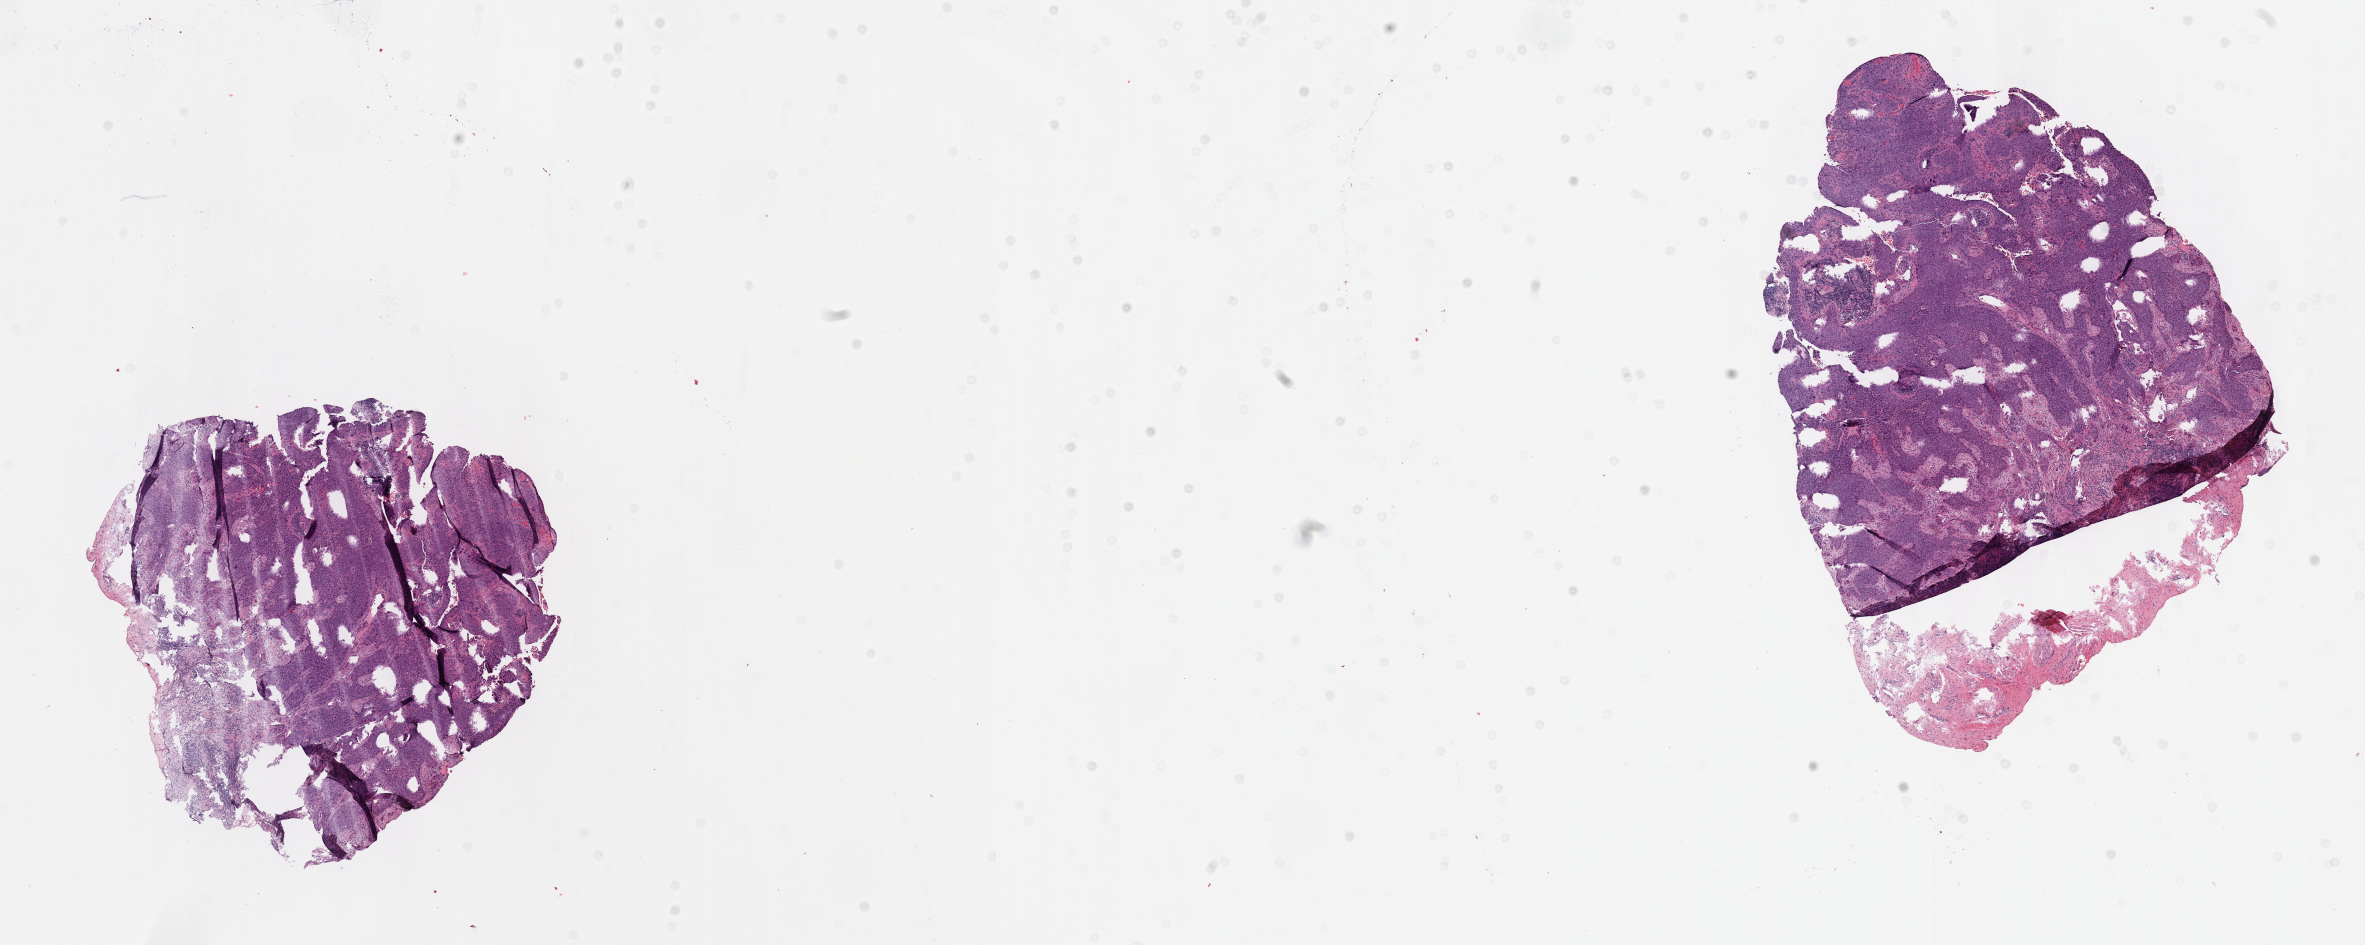
Digitized H&E tissue section (whole slide) — low-resolution overview of the scanned area, about 19.1 x 7.6 mm. Formalin-fixed paraffin-embedded (FFPE) diagnostic section. Sample: primary tumour, cervix. Patient: female, age at initial diagnosis 27 years. Histologic grade: G3 (poorly differentiated).
- FIGO stage: IB1
- histologic diagnosis: Squamous cell carcinoma, NOS (cervix uteri)